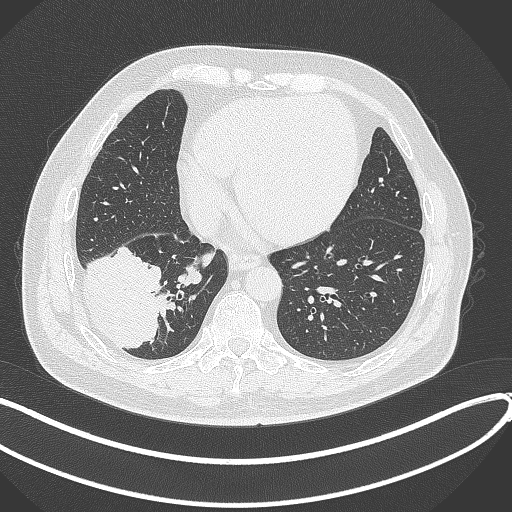
Chest CT, one axial slice. Position 114 of 360 along the scan axis. 120 kVp. Lung window (W 1500 / L -600 HU). 1 mm slice thickness. 512 × 512 image matrix, field of view 400 × 400 mm. Patient: male, 59 years.
Structures marked on this image (bounding box drawn by a radiologist):
- lung tumour (recorded histology: adenocarcinoma): box from (x=81, y=240) to (x=178, y=351) px